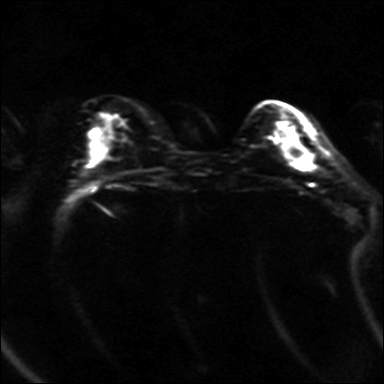
Breast MRI, one axial slice; slice 11 of 36 in the series (ordered by position); diffusion-weighted series; image 2 of 4 stored at this slice position (different b-values; order by instance number); 3 T; 384 × 384 image matrix, field of view 320 × 320 mm. Female patient.
Annotated regions visible in this slice (outlined manually by an expert reader):
- tumour on diffusion-weighted imaging: bounding box [x1, y1, x2, y2] px = [285, 138, 301, 162]